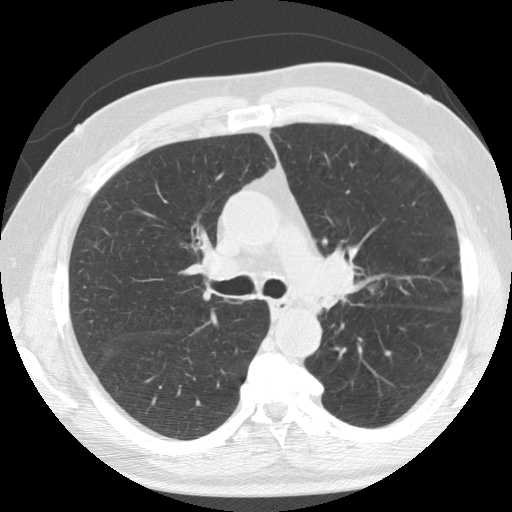
Low-dose screening chest CT, one axial slice. Position 85 of 133 along the scan axis. 120 kVp. Lung window (W 1500 / L -600 HU). 2.5 mm slice thickness. 512 × 512 image matrix, field of view 342 × 342 mm.
Outlined on this slice (manually delineated by an expert):
- lesion 1 (tumor, upper lobe of left lung): box from (x=319, y=254) to (x=353, y=308) px